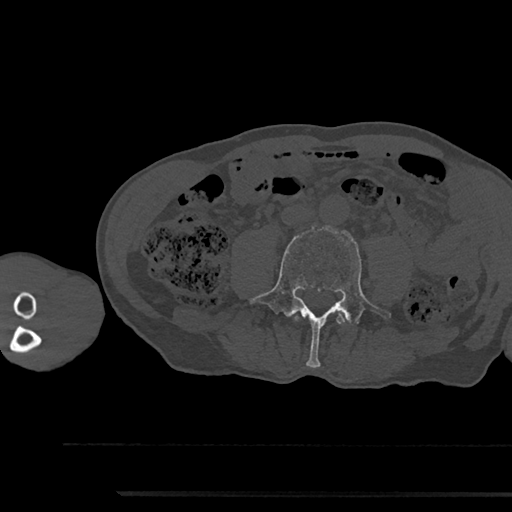
CT including the spine, one axial slice; position 424 of 797 along the scan axis; bone window (W 1800 / L 400 HU); 512 × 512 image matrix, field of view 367 × 367 mm. Patient: male, 79 years. Case-level facts recorded for this patient, not image findings: primary cancer: prostate.
Outlined on this slice (semi-automatic segmentation, software-assisted and operator-edited):
- L3 vertebra: bounding box [x1, y1, x2, y2] px = [295, 314, 344, 323]
- L4 vertebra: [249, 226, 391, 367]